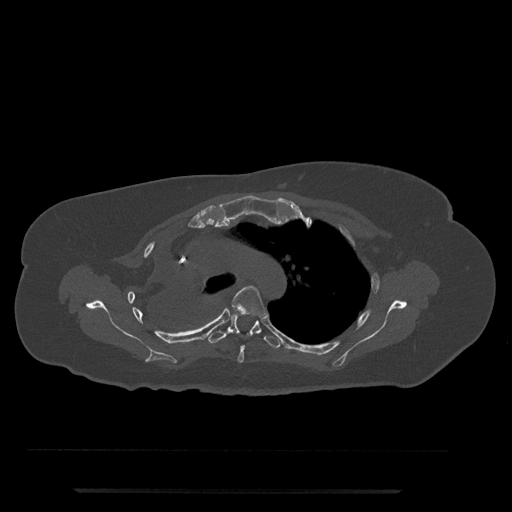
CT including the spine, one axial slice. Slice 565 of 797 in the series (ordered by position). Bone window (W 1800 / L 400 HU). 512 × 512 image matrix, field of view 440 × 440 mm. Female patient, age 51 years. Case-level facts recorded for this patient, not image findings: primary cancer: neuro; vertebrae with lytic lesions (as recorded): T8.
Outlined on this slice (semi-automatically segmented with operator editing):
- T4 vertebra: bounding box (x1, y1, x2, y2) in pixels: (226, 286, 267, 363)
- T5 vertebra: (206, 314, 282, 349)